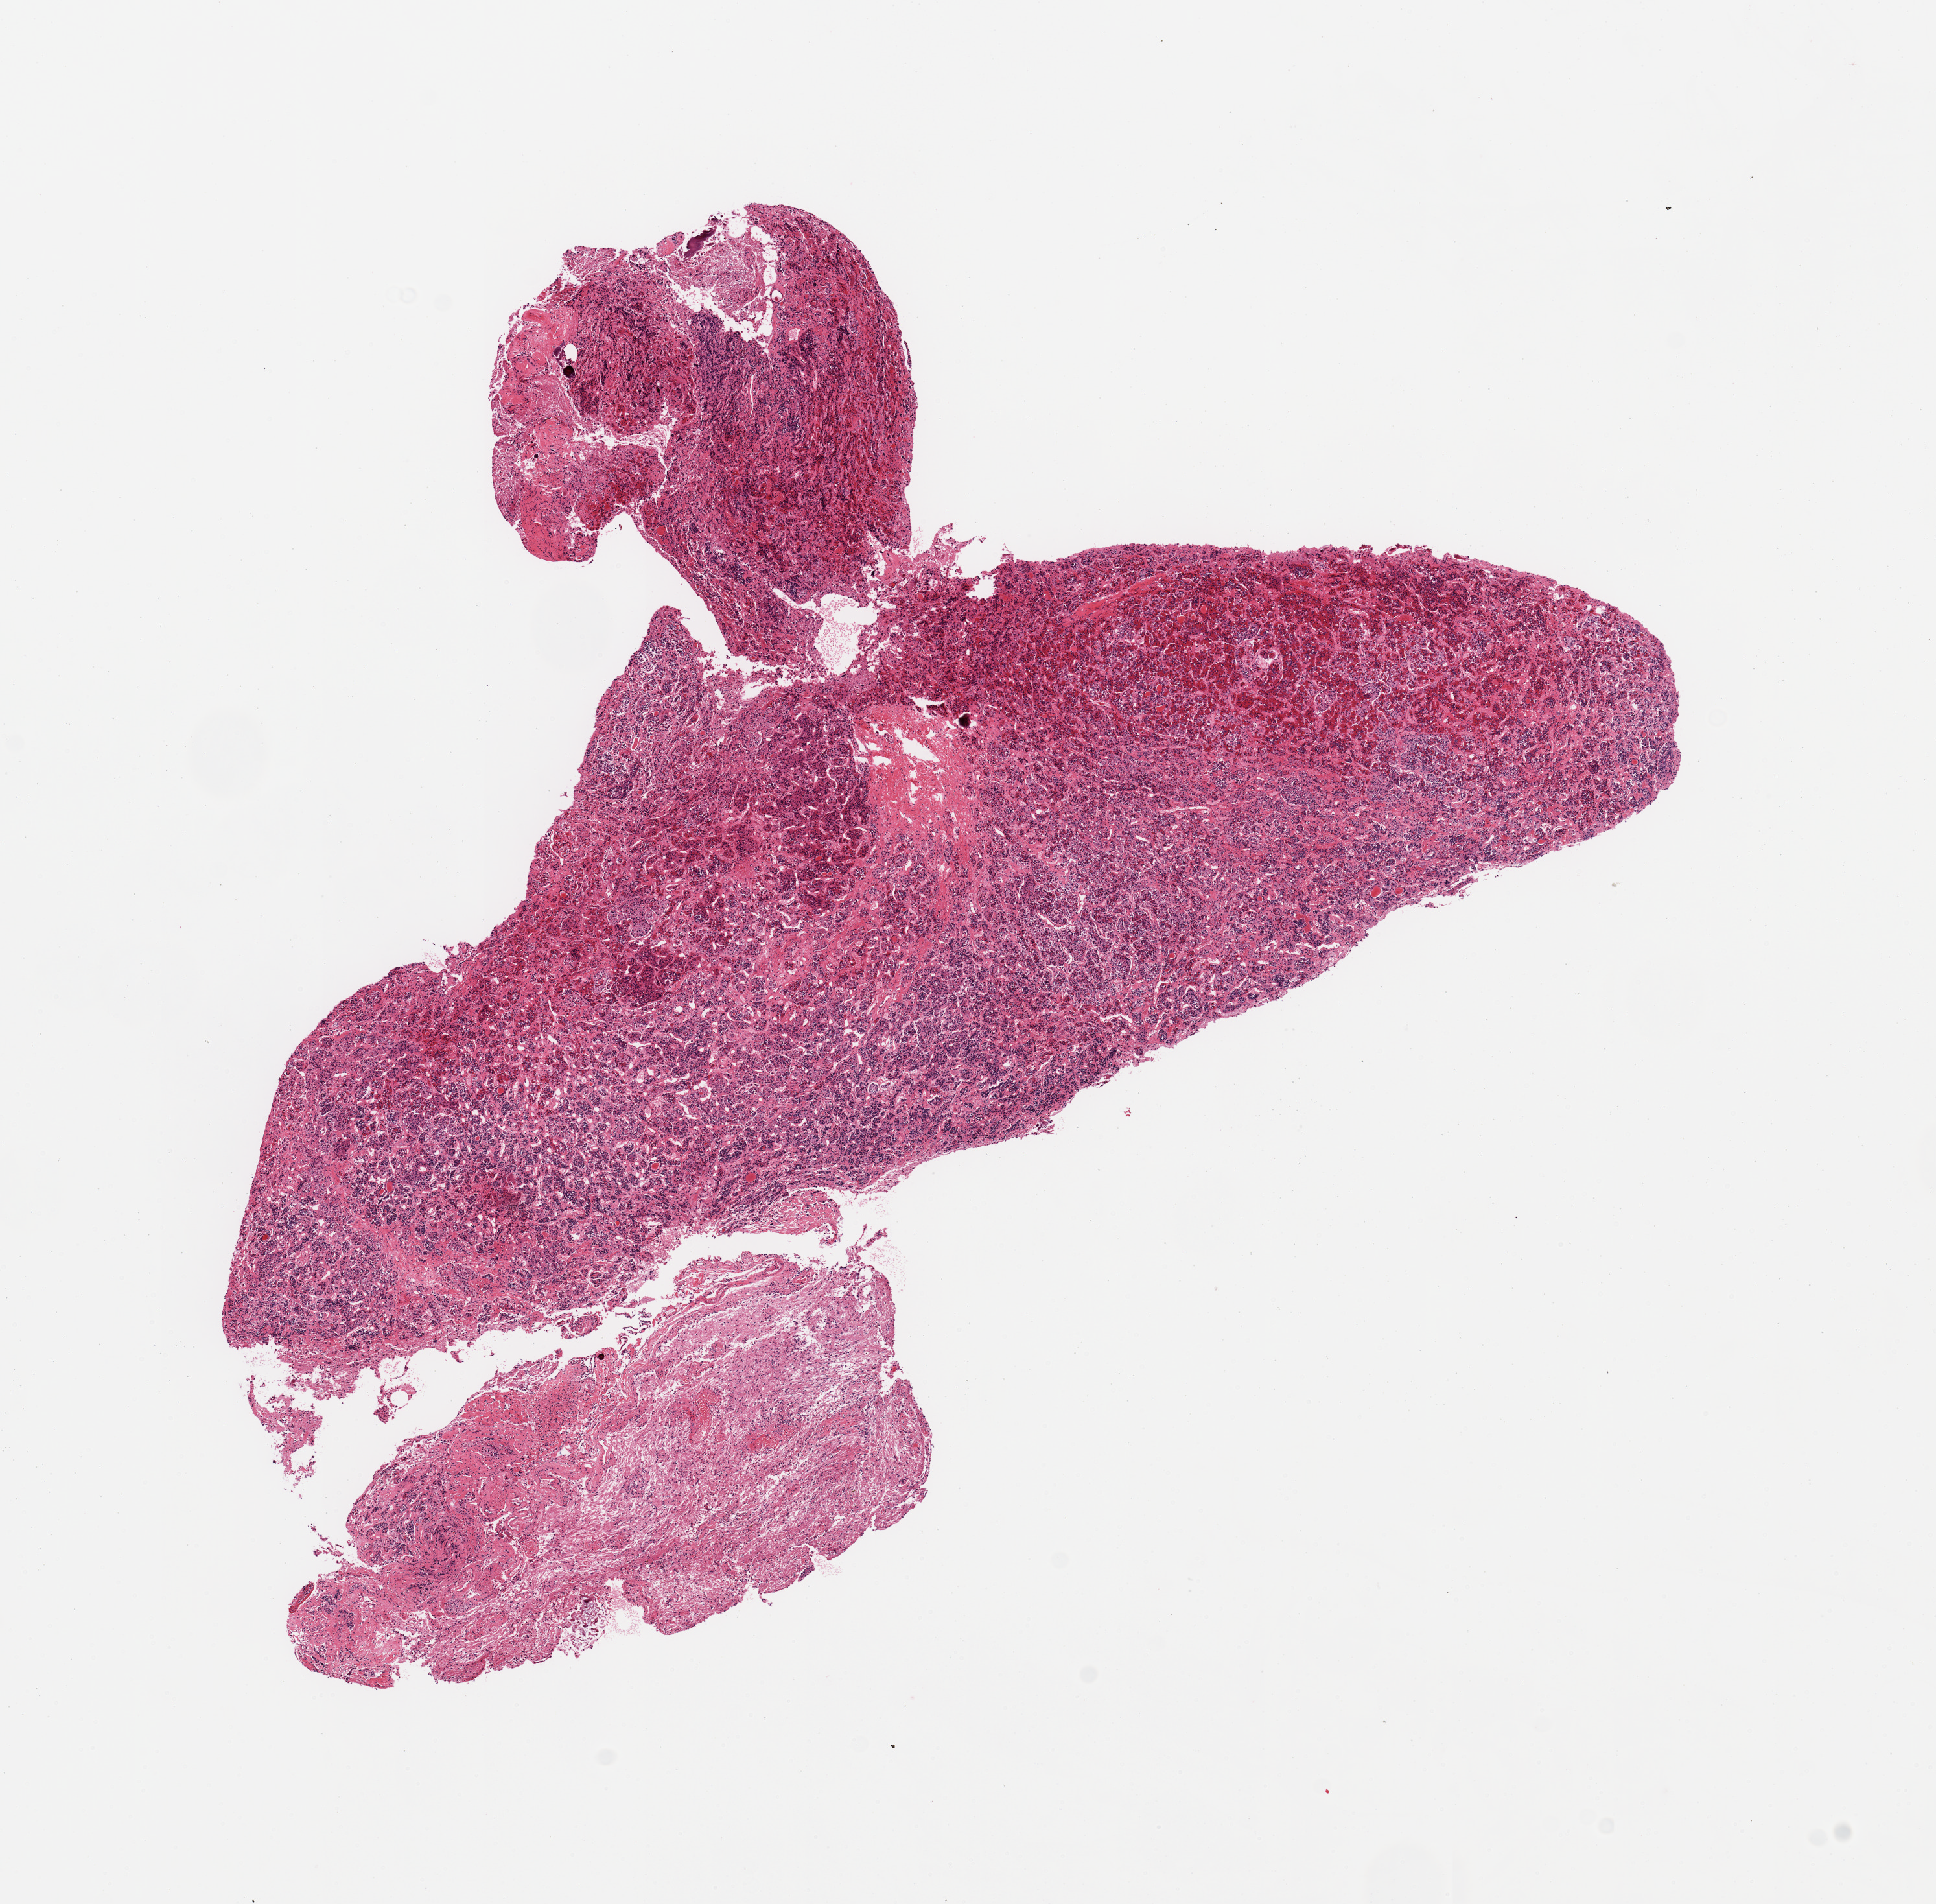
Digitized H&E-stained section, brightfield — whole scanned area (about 11.8 x 11.6 mm) shown as a low-resolution overview; PAXgene-fixed paraffin-embedded (PFPE) section; section of pituitary (target tissue); tissue donor sample. Donor: male.
Reviewer comment on this tissue sample: 2 pieces + fragments, mainly adenohypophysis, 4x2mm fragment of neurohypophysis.